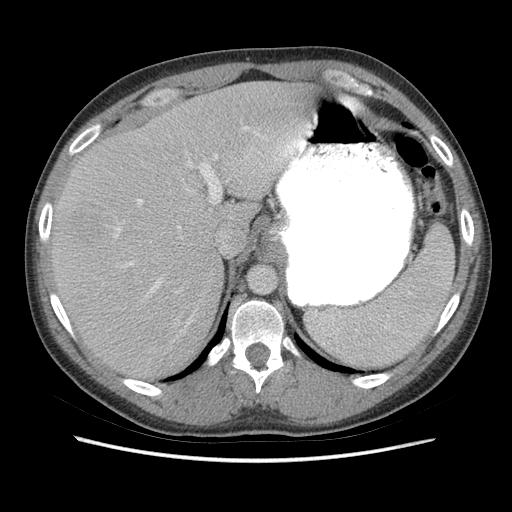
Contrast-enhanced abdominal CT (liver protocol), one axial slice; position 51 of 73 along the scan axis; reconstruction kernel STANDARD; 140 kVp; soft-tissue window (W 400 / L 40 HU); 512 × 512 image matrix, field of view 360 × 360 mm. From the clinical record (not read from this slice): diagnosis: hepatocellular carcinoma (patient treated with transarterial chemoembolisation; whether this scan precedes or follows treatment is not stated here); TNM stage (as recorded): Stage-IIIA; Child-Pugh class: A.
Outlined on this slice (semi-automatically segmented with operator editing):
- liver parenchyma outside the tumour (the mass and vessels are separate outlines, so this box may not span the whole liver): box from (x=50, y=82) to (x=316, y=380) px
- mass: (x=59, y=203)–(x=112, y=248)
- liver vessels: (x=113, y=117)–(x=316, y=325)